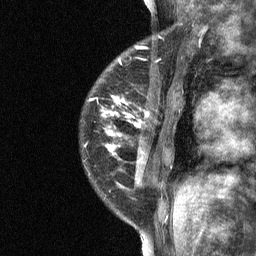
Breast MRI (dynamic contrast-enhanced), one sagittal slice; position 17 of 64 along the scan axis; dynamic contrast-enhanced study with each time point stored as its own series, time point 2 of 3 at this slice position (early post-contrast, ordered by acquisition time); 1.5 T; TE 4.8 ms, TR 27 ms; 2 mm slice thickness; 256 × 256 image matrix. Female patient, age 34 years. From the clinical record (not read from this slice): setting: breast cancer imaged before/during neoadjuvant chemotherapy; receptor status: HR-positive, HER2-negative.
Structures marked on this image (semi-automatic segmentation, software-assisted and operator-edited):
- analysis volume of interest (the breast-tissue region the enhancement analysis was run in; not a lesion): bounding box (x1, y1, x2, y2) in pixels: (80, 44, 181, 191)
- tumour enhancement mask (voxels above the 90 % enhancement threshold inside the analysis volume of interest): (106, 47, 147, 152)